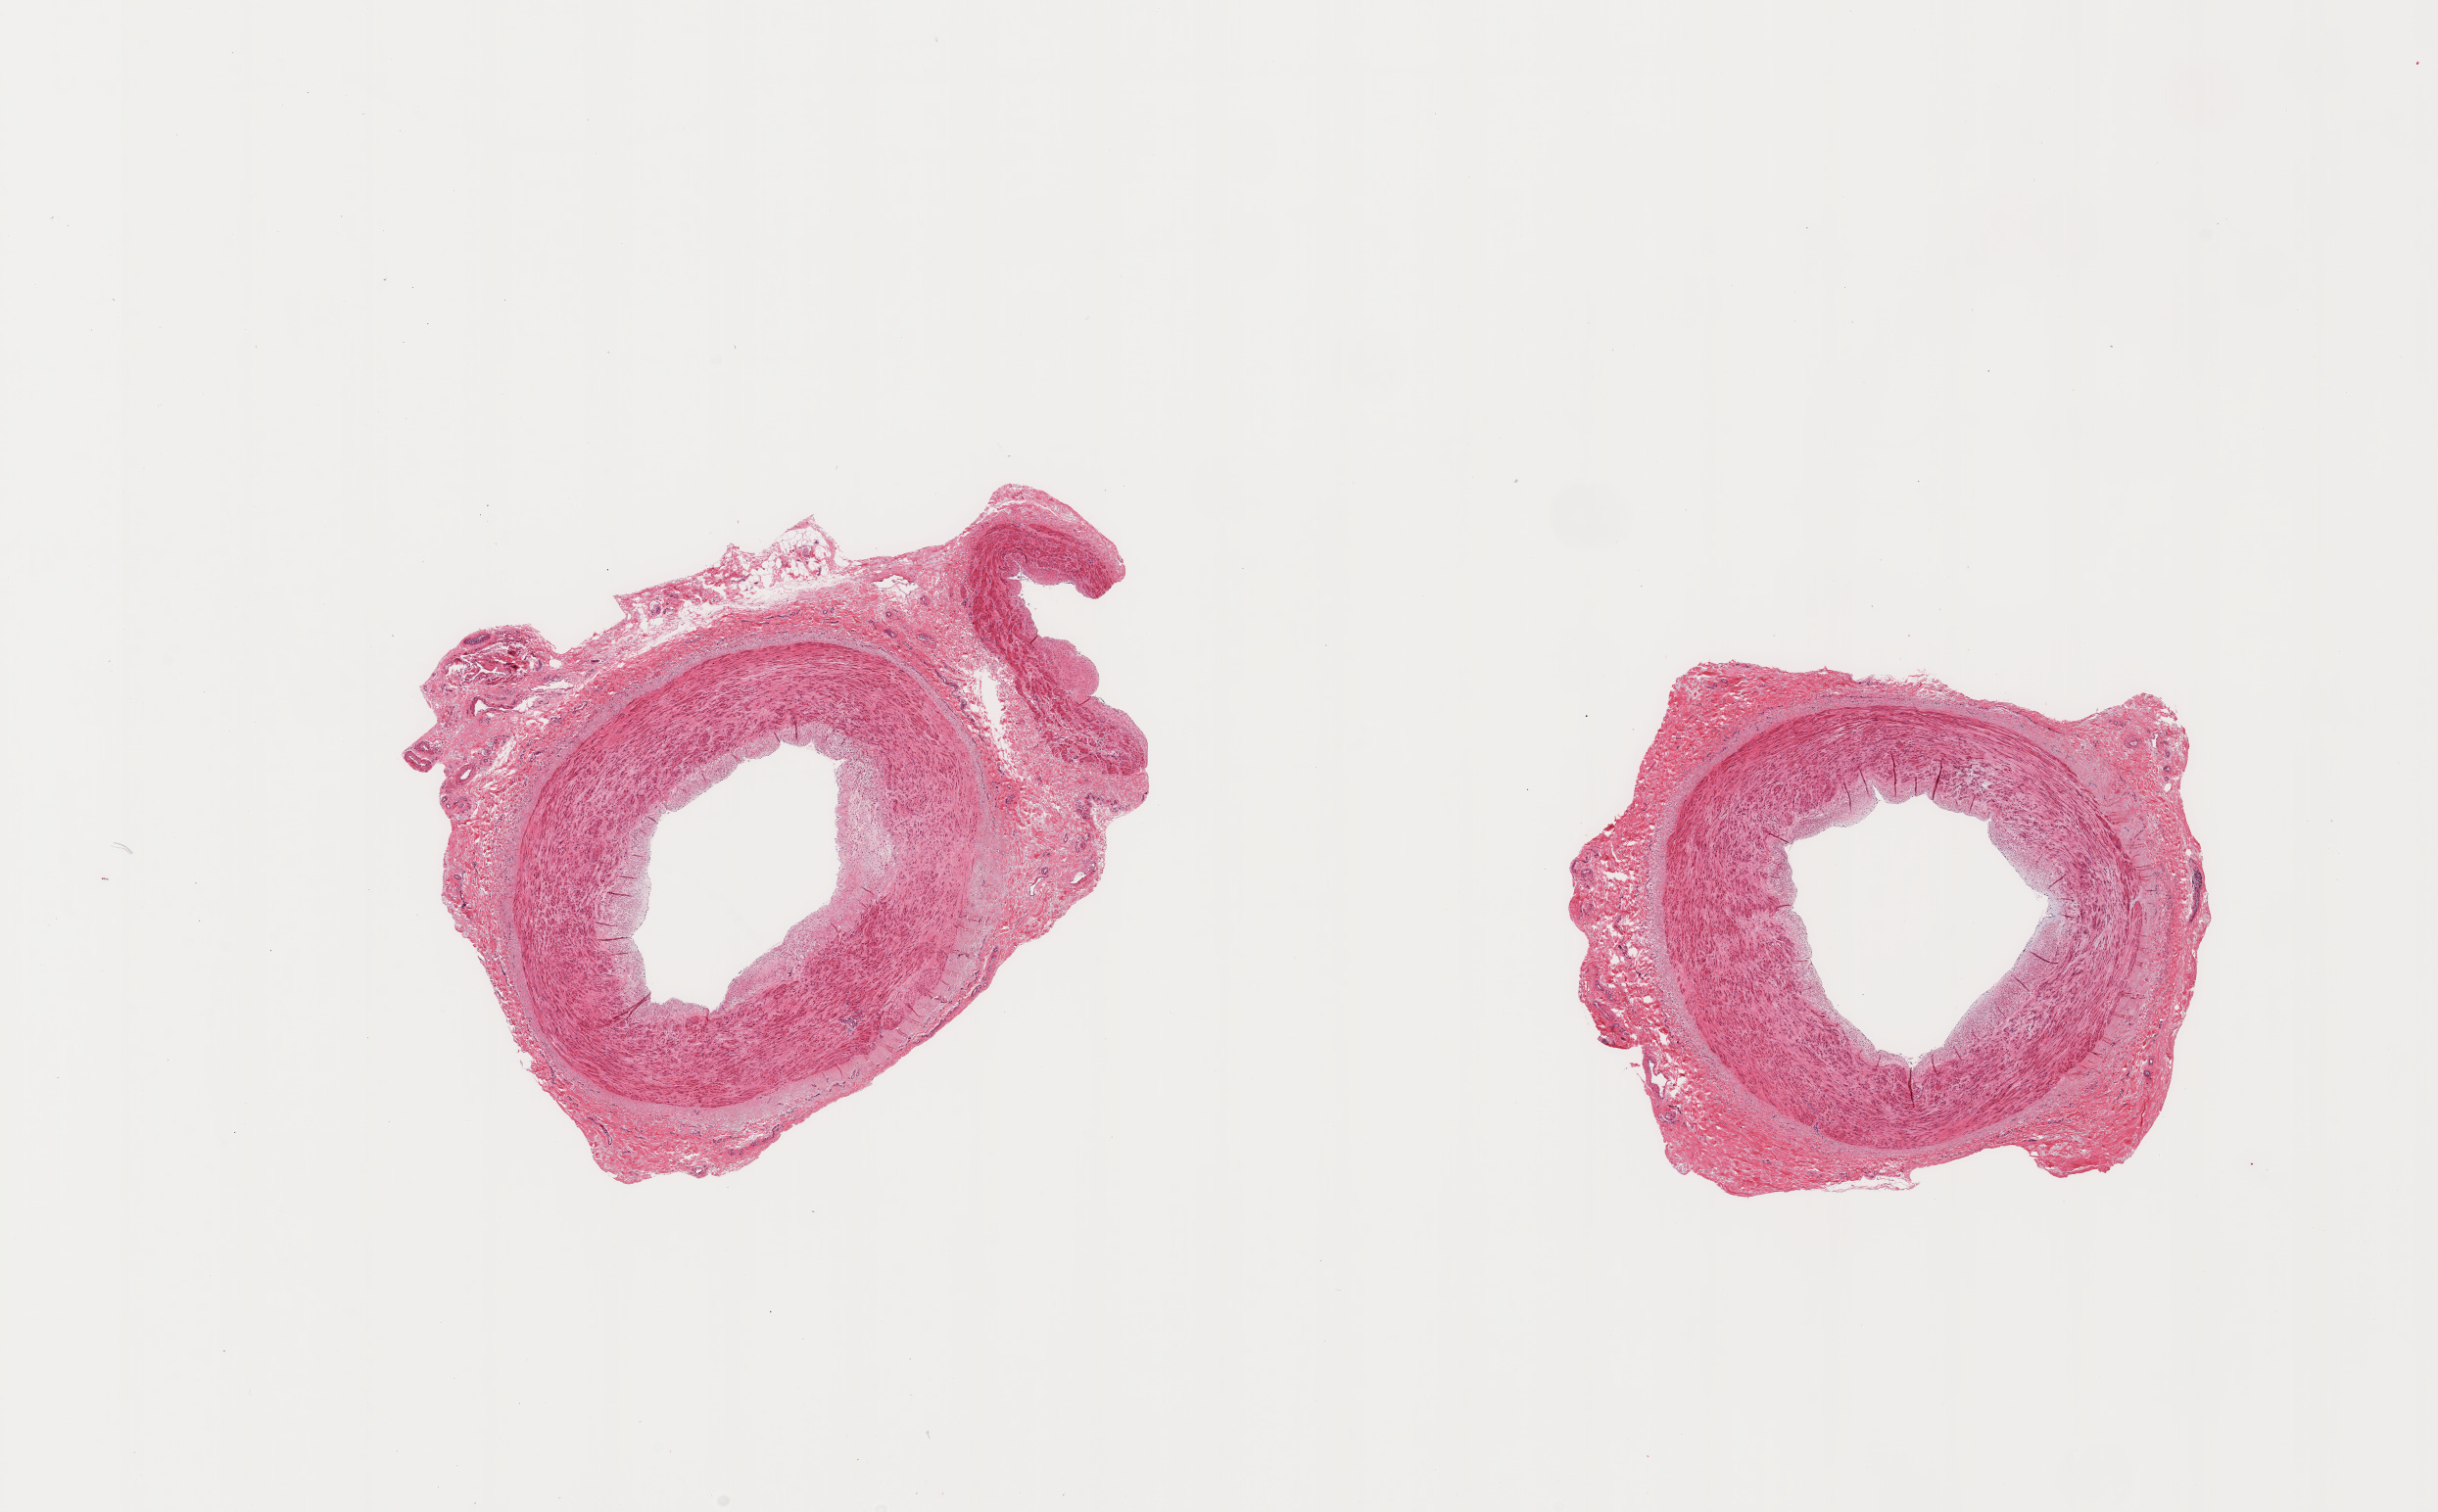
Hematoxylin and eosin (H&E) whole-slide image — low-resolution overview of the scanned area, about 19.7 x 12.2 mm (acquisition: 20x scan). PAXgene-fixed paraffin-embedded (PFPE) section. Section of tibial artery (target tissue). Donor tissue sample. Donor: male.
Reviewer comment on this tissue sample: 2 pieces, rims of fat/fibrous tissue up to ~1mm.